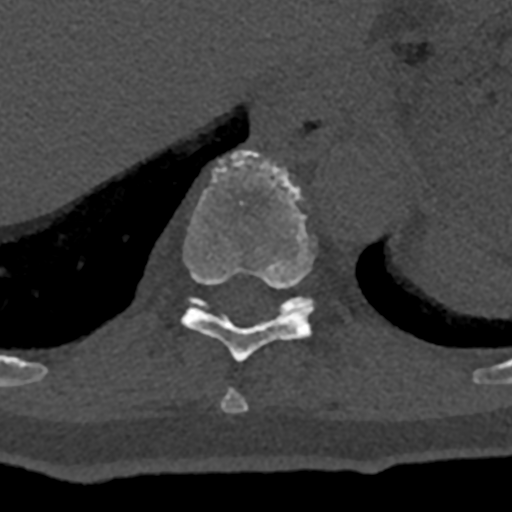
CT including the spine, one axial slice; slice 595 of 797 in the series (ordered by position); bone window (W 1800 / L 400 HU); 0.5 mm slice thickness; 512 × 512 image matrix, field of view 160 × 160 mm. Male patient, age 74 years. From the clinical record (not read from this slice): primary cancer: renal.
Structures marked on this image (semi-automatically segmented with operator editing):
- T10 vertebra: bounding box <181,150,315,362> (left, top, right, bottom; pixels)
- T11 vertebra: <189,296,314,315>
- T9 vertebra: <221,388,248,413>